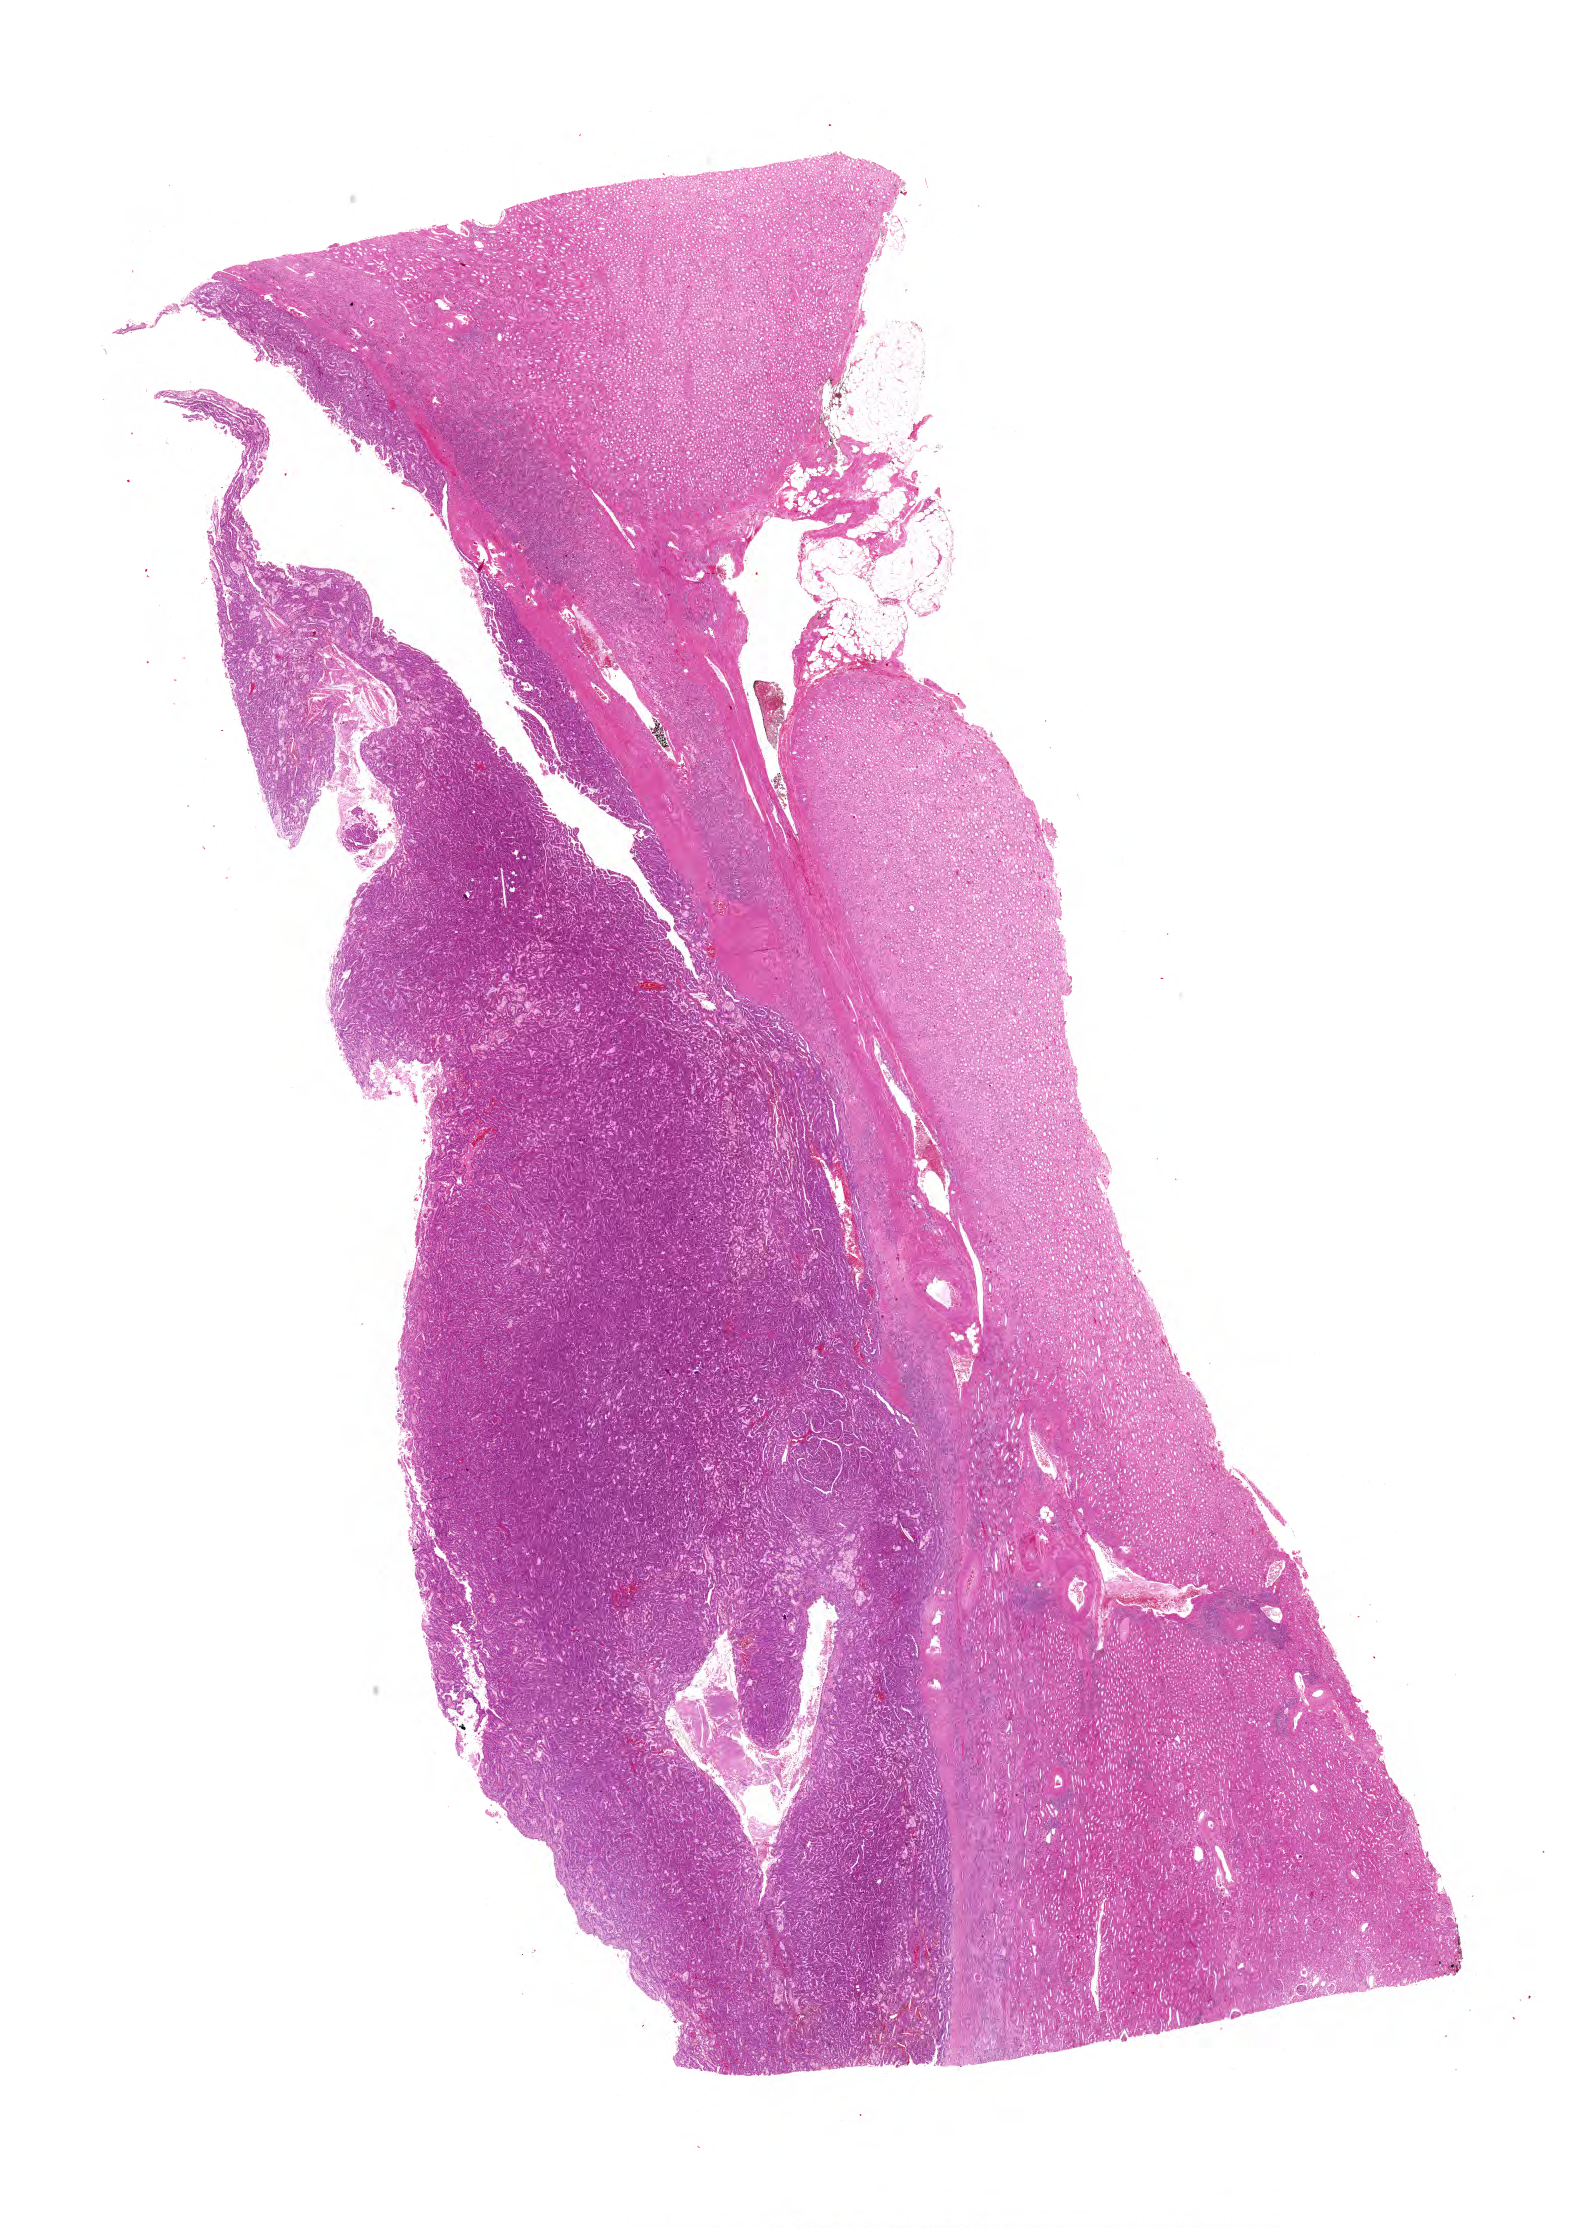
H&E-stained whole-slide image, whole scanned area (about 19.8 x 27.7 mm, acquisition: 40x scan) shown as a low-resolution overview; FFPE section; kidney, primary tumour sample. Patient: male, age at initial diagnosis 62 years.
Laterality: right. Diagnosis: Papillary adenocarcinoma, NOS.